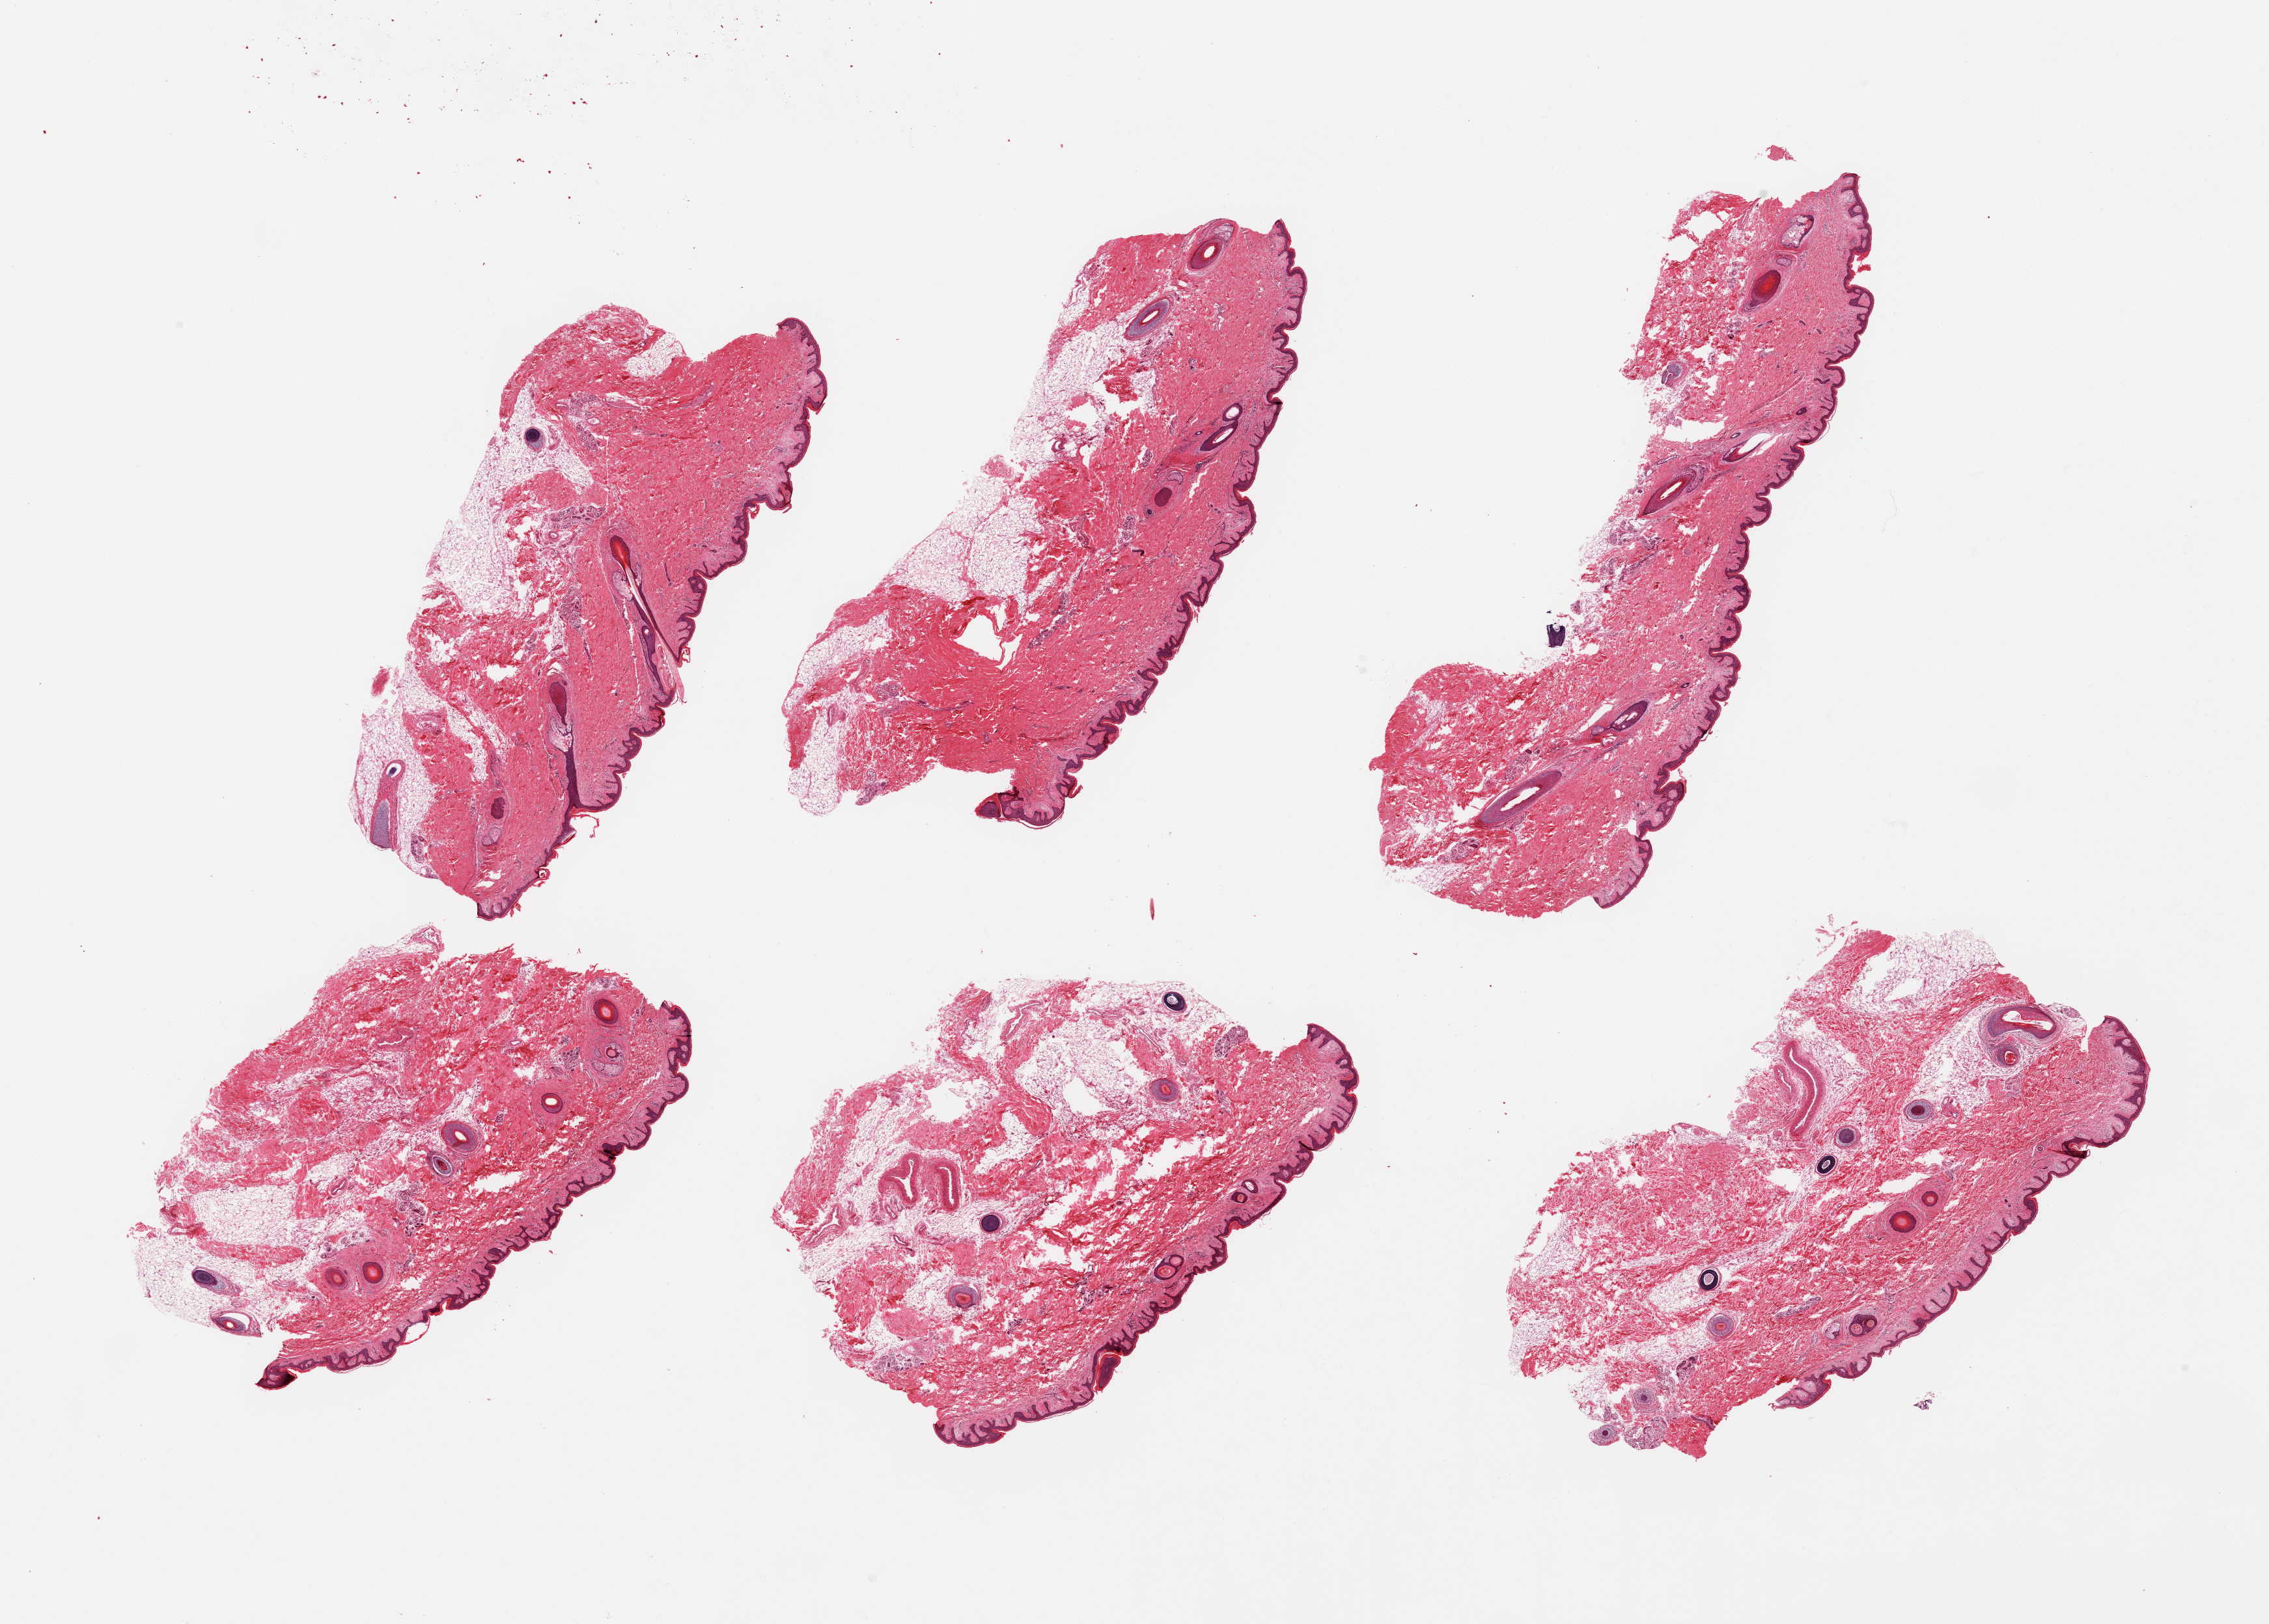
Digitized haematoxylin and eosin-stained section, a low-resolution overview of the entire scanned area, about 27.6 x 19.7 mm (from a 20x scan), PAXgene-fixed paraffin-embedded (PFPE) section, section of skin of suprapubic region (target tissue), donor tissue sample. Donor: male.
Pathologist's review note for this sample: 6 pieces; hair bearing skin; 10% to 20% internal (periadnexal) and external fat.